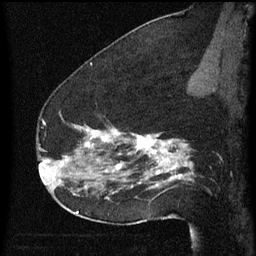
Breast MRI (dynamic contrast-enhanced), one sagittal slice; position 40 of 60 along the scan axis; dynamic contrast-enhanced series, image 2 of 3 at this slice position (ordered by acquisition); 1.5 T; TE 4.2 ms, TR 8 ms; 2 mm slice thickness; 256 × 256 image matrix, field of view 180 × 180 mm. Patient: female, 52 years.
Outlined on this slice (semi-automatically segmented with operator editing):
- analysis volume of interest (the breast-tissue region the enhancement analysis was run in; not a lesion): bounding box <54,112,178,207> (left, top, right, bottom; pixels)
- tumour enhancement mask (voxels above the 70 % enhancement threshold inside the analysis volume of interest): <64,130,178,199>